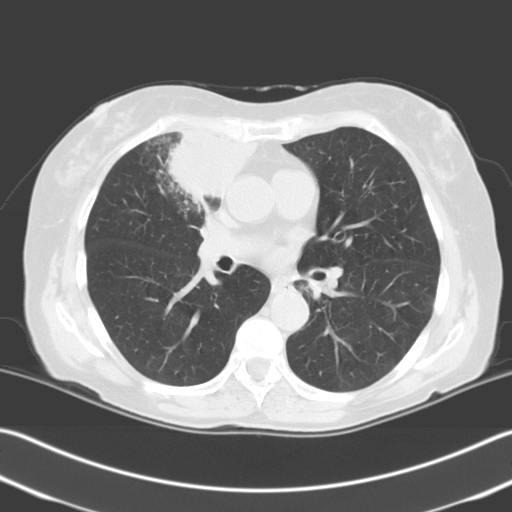
Low-dose screening chest CT, one axial slice. Position 120 of 204 along the scan axis. 140 kVp. Lung window (W 1500 / L -600 HU). 3.2 mm slice thickness. 512 × 512 image matrix.
Structures marked on this image (manually delineated by an expert):
- lesion 1 (tumor, upper lobe of right lung): bounding box (x1, y1, x2, y2) in pixels: (167, 131, 257, 208)